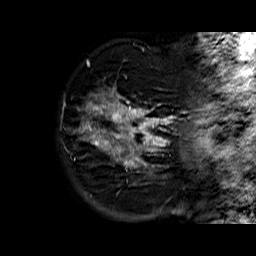
Breast MRI (dynamic contrast-enhanced), one sagittal slice; position 11 of 60 along the scan axis; dynamic contrast-enhanced series, time point 2 of 6 at this slice position (early post-contrast); 1.5 T; TE 6.3 ms, TR 32.4 ms; 4 mm slice thickness; 256 × 256 image matrix, field of view 200 × 200 mm. Female patient. From the clinical record (not read from this slice): setting: breast cancer imaged before/during neoadjuvant chemotherapy; receptor status: HR-positive, HER2-negative.
Annotated regions visible in this slice (semi-automatic segmentation, software-assisted and operator-edited):
- analysis volume of interest (the breast-tissue region the enhancement analysis was run in; not a lesion): box from (x=74, y=73) to (x=176, y=183) px
- tumour enhancement mask (voxels above the 100 % enhancement threshold inside the analysis volume of interest): (x=78, y=88)–(x=175, y=172)